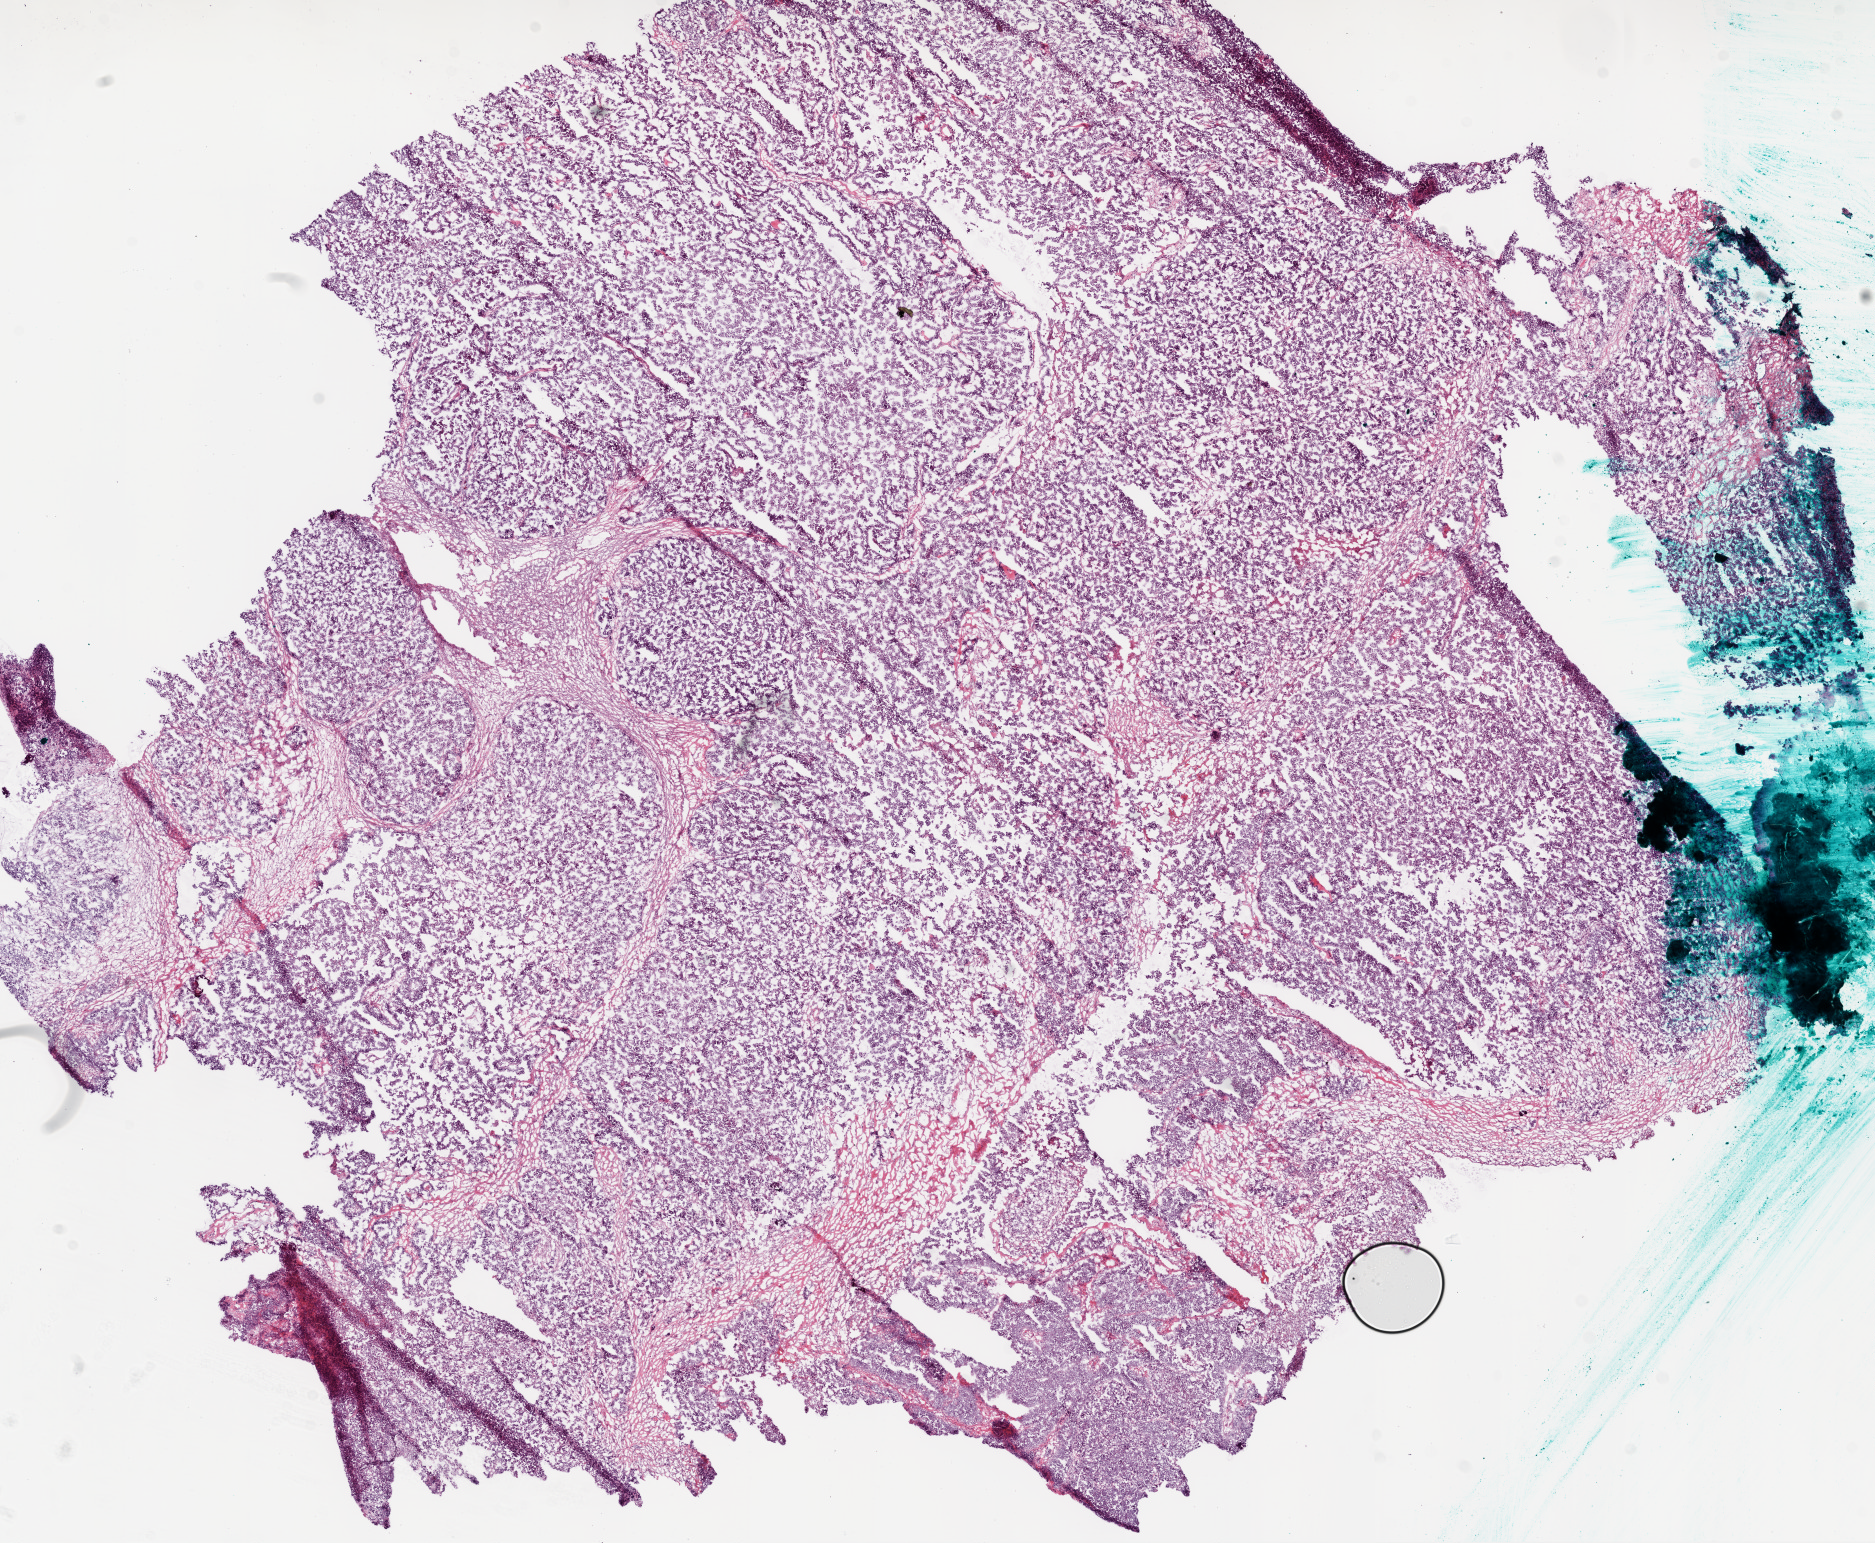
H&E-stained whole-slide image, whole scanned area (about 15.0 x 12.4 mm) shown as a low-resolution overview. Frozen section from the bottom of the tissue portion. Primary tumour sample from the ovary. Female, age 74 years at initial diagnosis. Histologic grade: G3 (poorly differentiated). Composition of this section per pathologist review: tumour cells 90%, tumour nuclei 90%, normal cells 0%, stromal cells 9%, necrosis 1%.
• diagnosis: Serous cystadenocarcinoma, NOS
• FIGO stage: IIIC
• laterality: bilateral